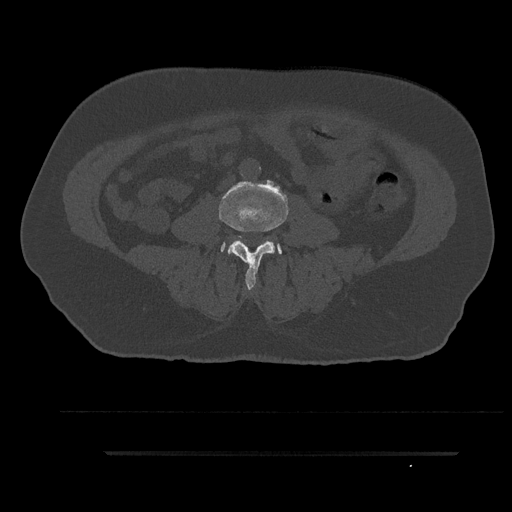
CT including the spine, one axial slice; slice 19 of 797 in the series (ordered by position); reconstruction kernel Br40s/3; 120 kVp; bone window (W 1800 / L 400 HU); 512 × 512 image matrix, field of view 432 × 432 mm. Patient: male, 63 years. Case-level facts recorded for this patient, not image findings: primary cancer: renal.
Outlined on this slice (semi-automatic segmentation, software-assisted and operator-edited):
- L3 vertebra: bounding box (x1, y1, x2, y2) in pixels: (219, 185, 288, 291)
- L4 vertebra: (221, 241, 282, 255)